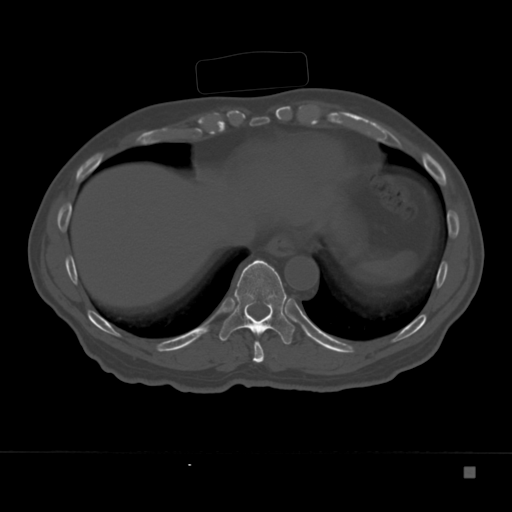
CT including the spine, one axial slice. Position 175 of 332 along the scan axis. Bone window (W 1800 / L 400 HU). 1.5 mm slice thickness. 512 × 512 image matrix, field of view 389 × 389 mm. Male patient, age 72 years. Case-level facts recorded for this patient, not image findings: primary cancer: skeletal.
Annotated regions visible in this slice (semi-automatically segmented with operator editing):
- T10 vertebra: bounding box (x1, y1, x2, y2) in pixels: (219, 260, 295, 345)
- T9 vertebra: (242, 327, 265, 363)